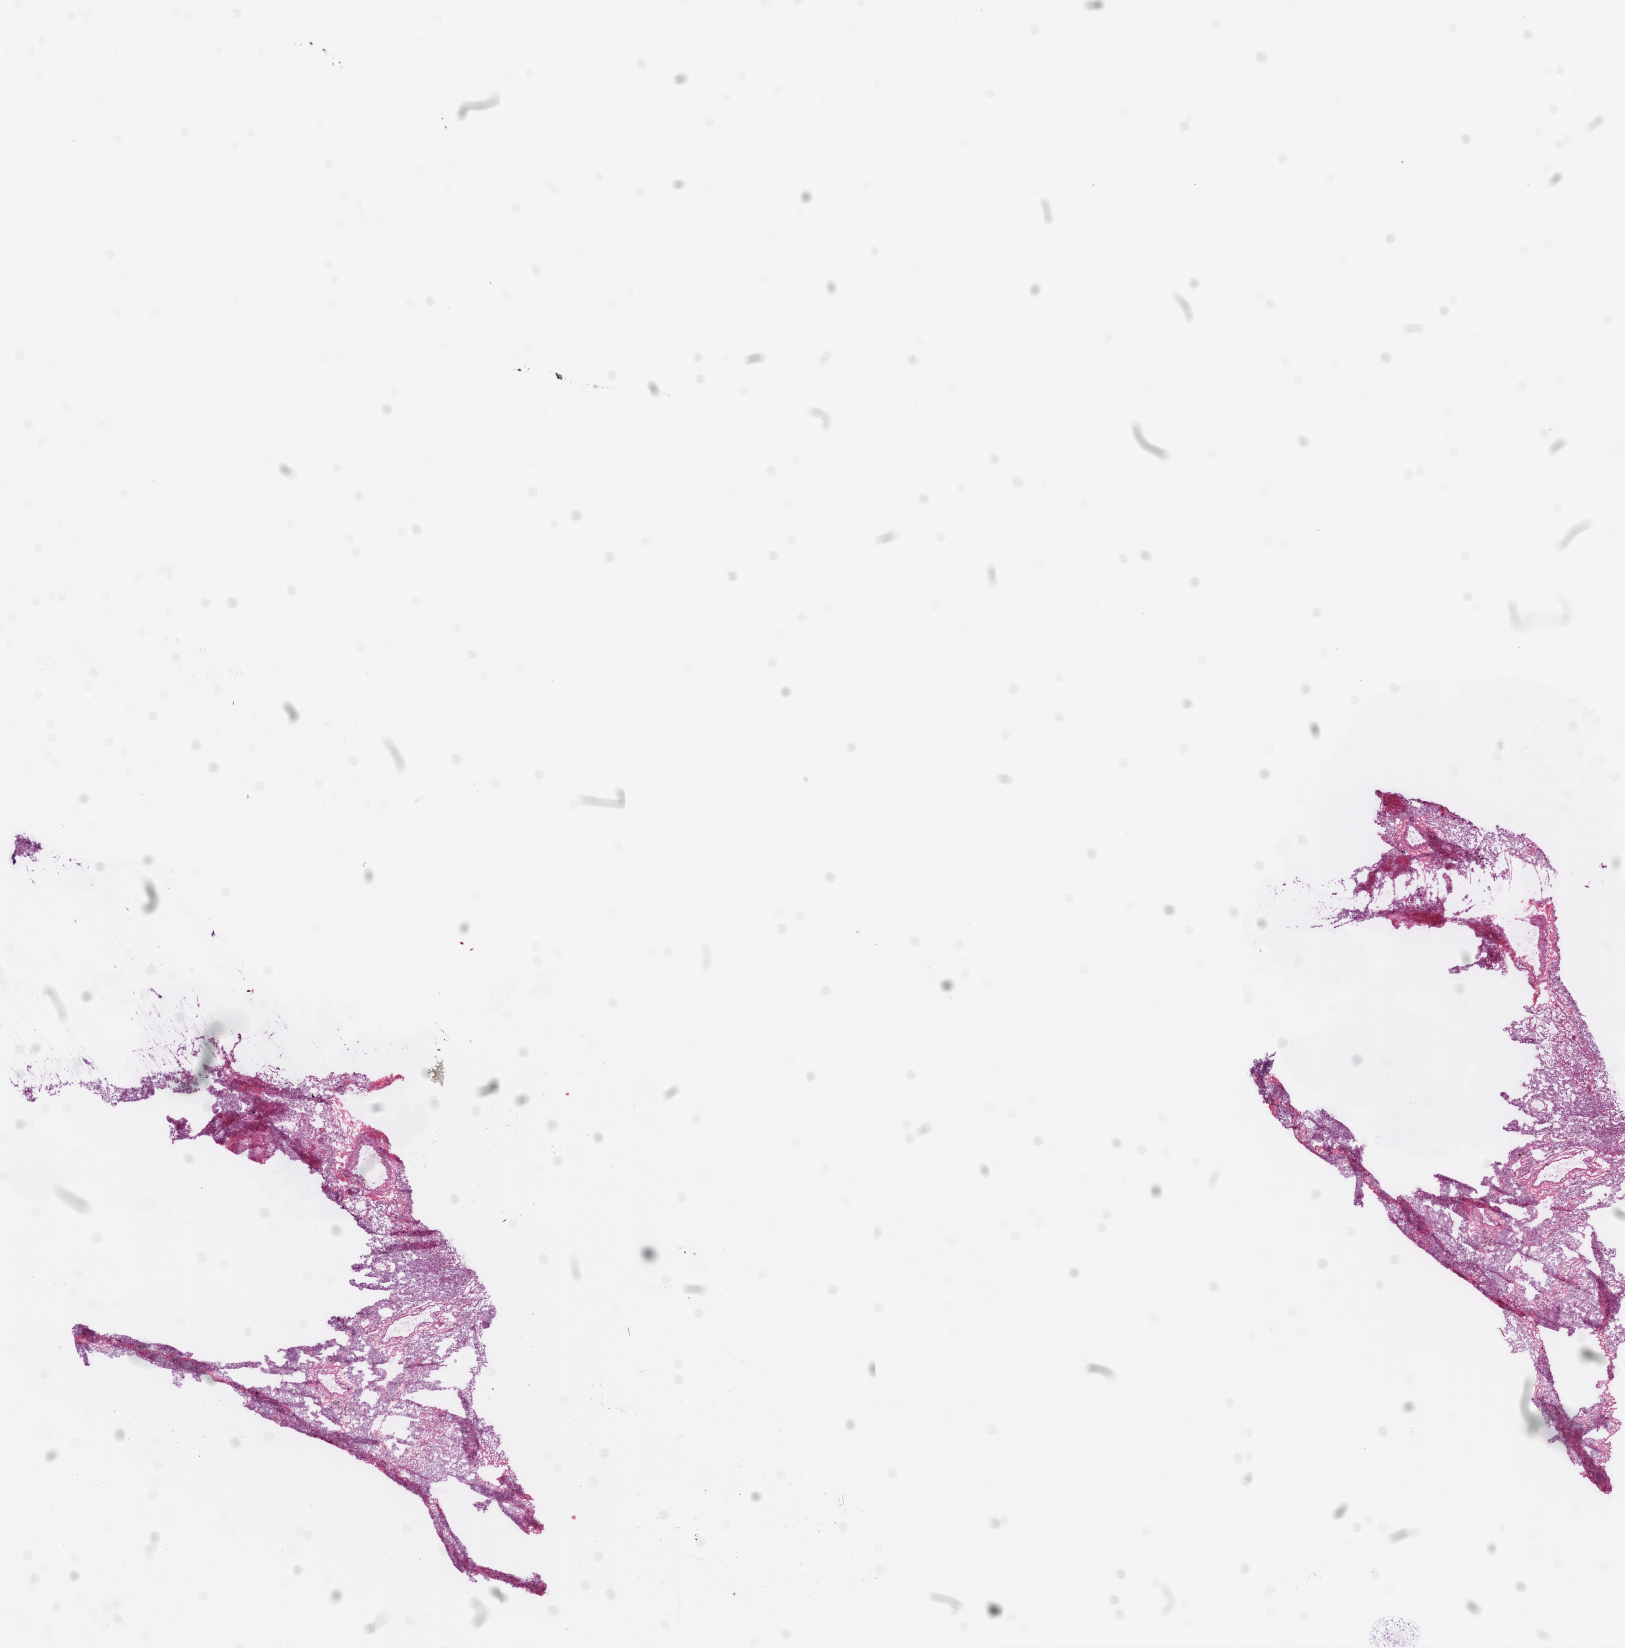
Whole-slide histology image, Hematoxylin and eosin (H&E) stained, shown as a low-resolution overview of the whole scanned area (about 13.0 x 13.2 mm, slide scanned at 20x), frozen section from the top of the tissue portion, solid tissue normal (non-tumour tissue) sample from the lung. Patient: male, age at initial diagnosis 71 years.
This section: solid tissue normal (non-tumour) sample from the same patient. Patient diagnosis: Squamous cell carcinoma, NOS (upper lobe, lung).